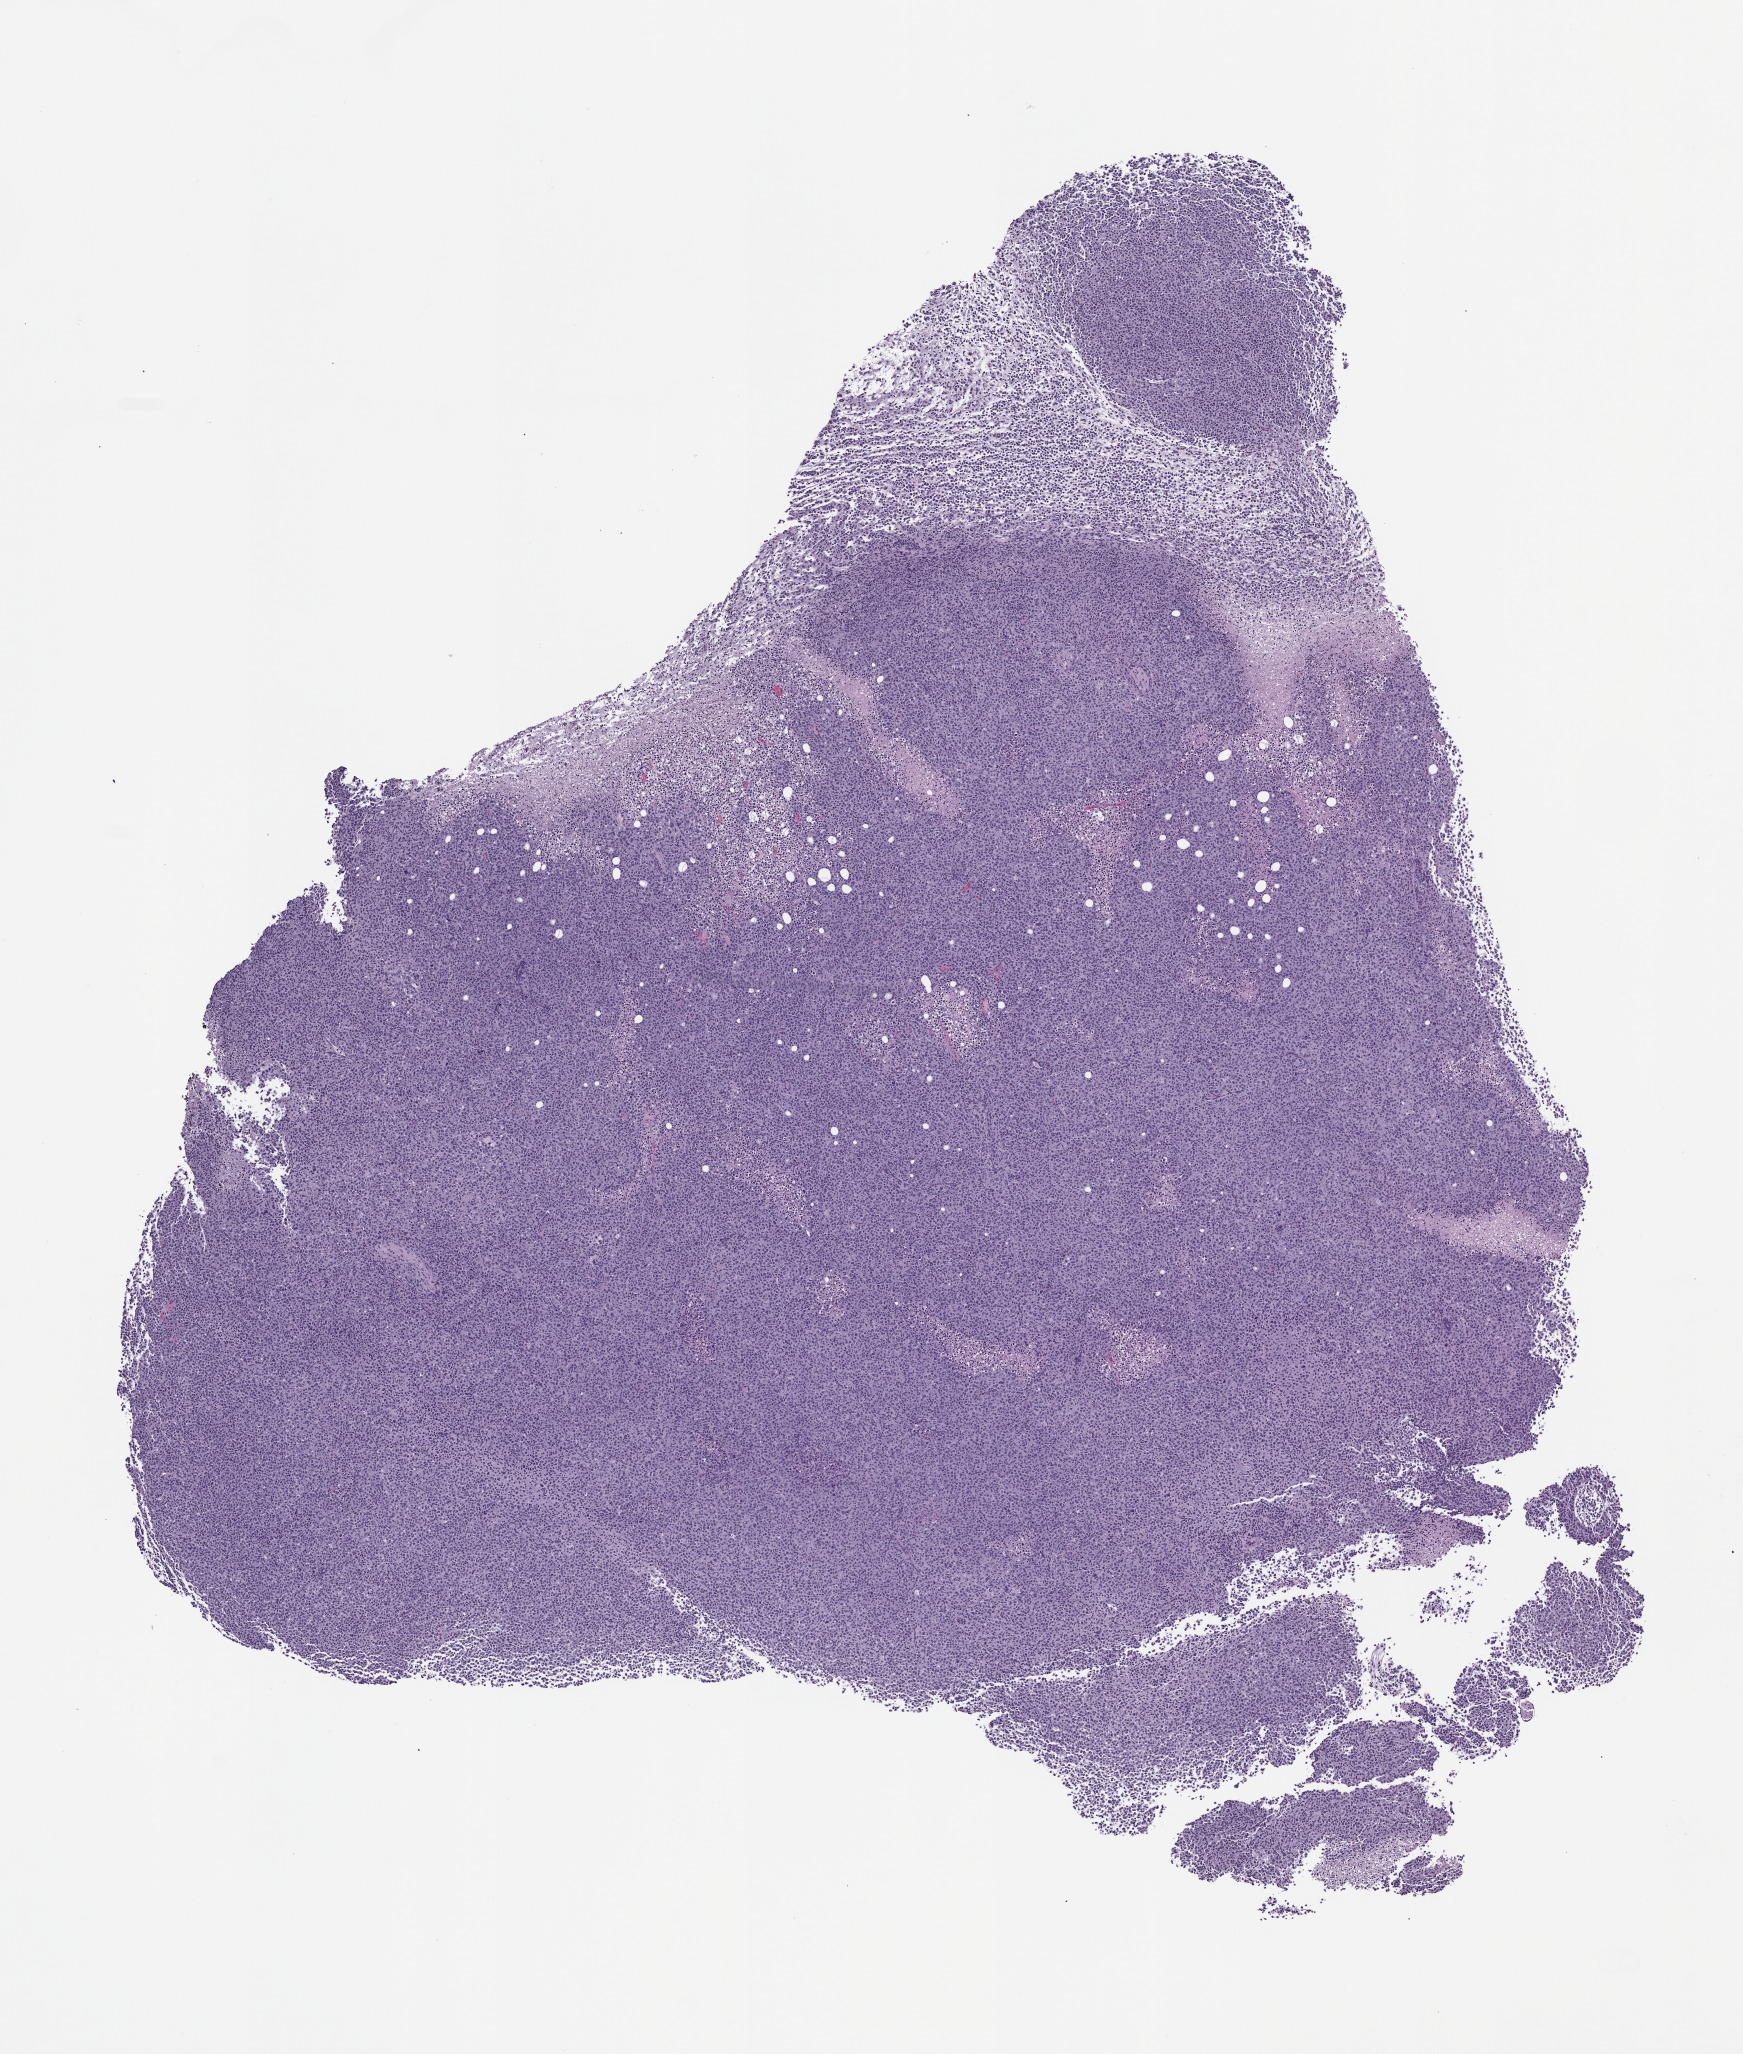
H&E whole-slide image of a patient-derived xenograft (PDX) tumor grown in a mouse — shown as a low-resolution overview of the whole scanned area (about 7.0 x 8.3 mm).
Specimen: formalin-fixed, paraffin-embedded (FFPE) tissue.